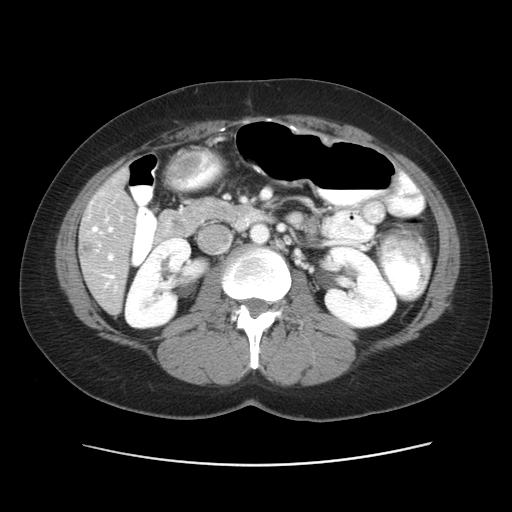
Contrast-enhanced abdominal CT, one axial slice. Slice 21 of 52 in the series (ordered by position). Reconstruction kernel STANDARD. 120 kVp. Soft-tissue window (W 400 / L 40 HU). 5 mm slice thickness. 512 × 512 image matrix, field of view 362 × 362 mm. Female patient, age 48 years. Case-level facts recorded for this patient, not image findings: diagnosis: colorectal cancer liver metastases, imaged before liver resection; multiple liver metastases: yes; largest metastasis: 4.5 cm.
Structures marked on this image (outlined manually by an expert reader):
- hepatic veins: bounding box [x1, y1, x2, y2] px = [92, 217, 123, 279]
- liver: [80, 173, 136, 312]
- portal vein (with intrahepatic branches): [108, 227, 114, 261]
- liver metastasis: [85, 245, 94, 254]